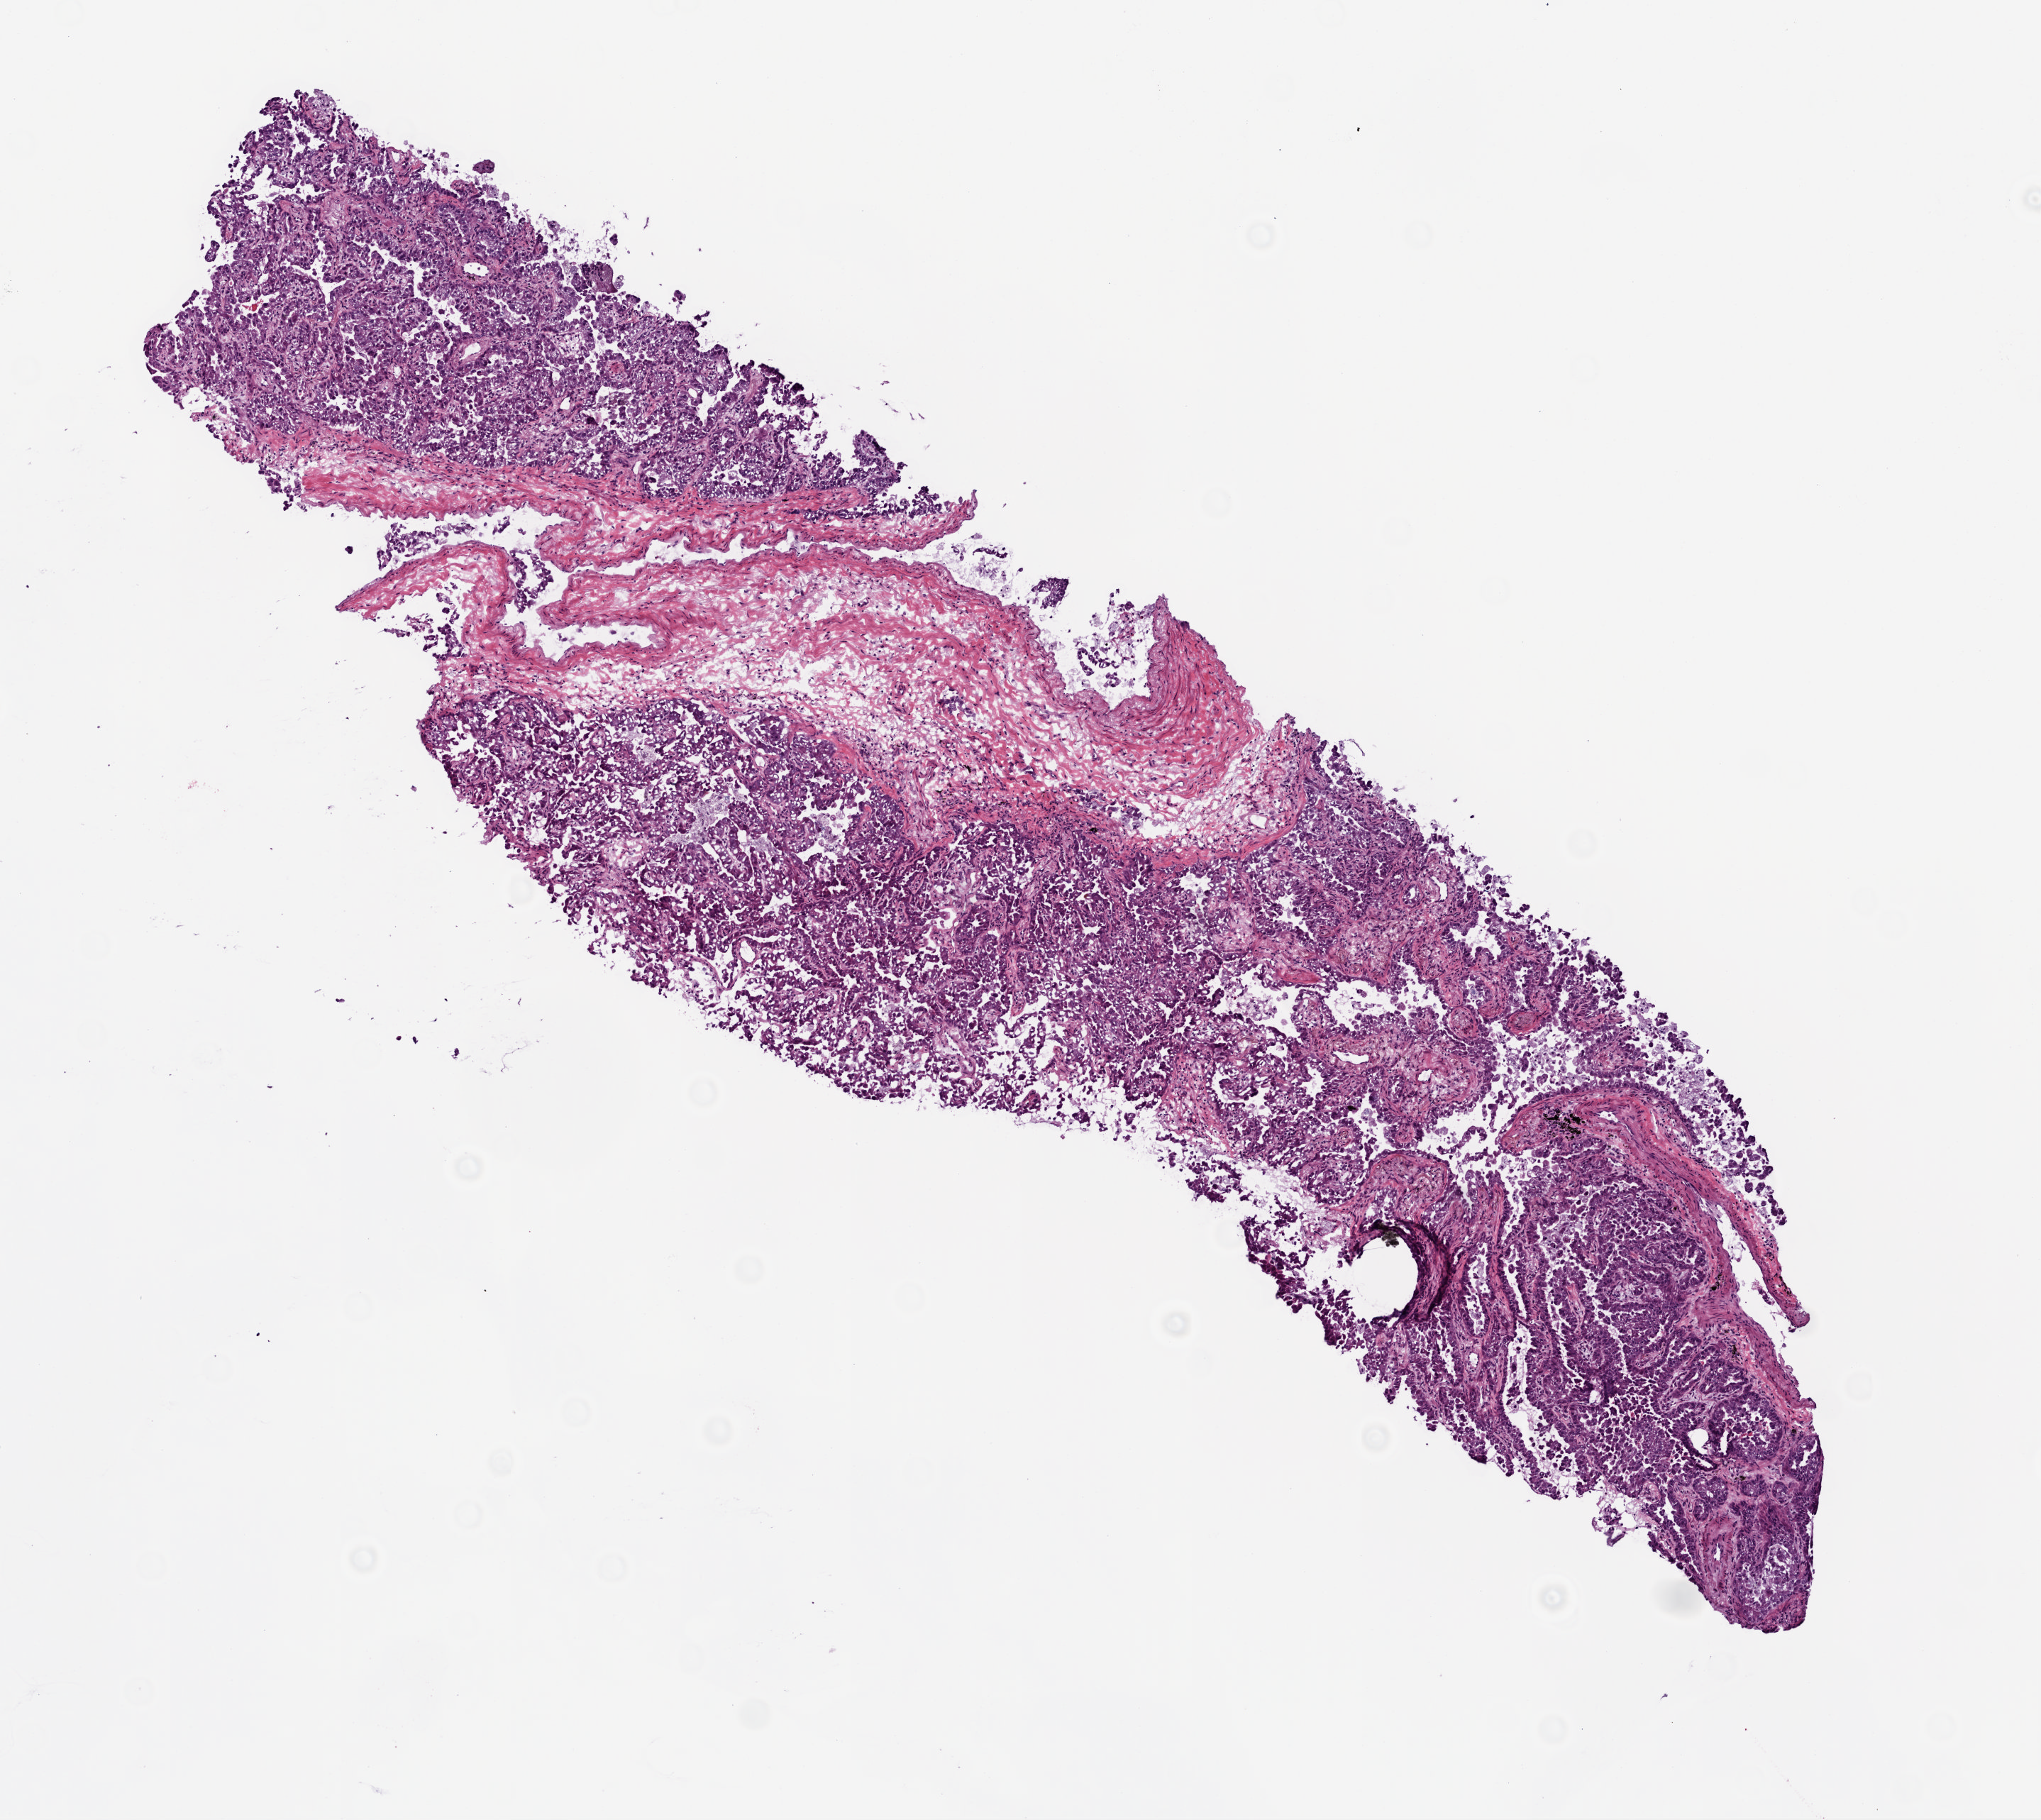
Digitized Hematoxylin and eosin (H&E) stained tissue section (whole slide), low-resolution overview of the scanned area, about 5.8 x 5.2 mm (slide scanned at 20x); frozen section from the bottom of the tissue portion; sample: primary tumour, lung. Male patient; age at initial diagnosis 64 years.
Diagnosis: Adenocarcinoma with mixed subtypes (middle lobe, lung).